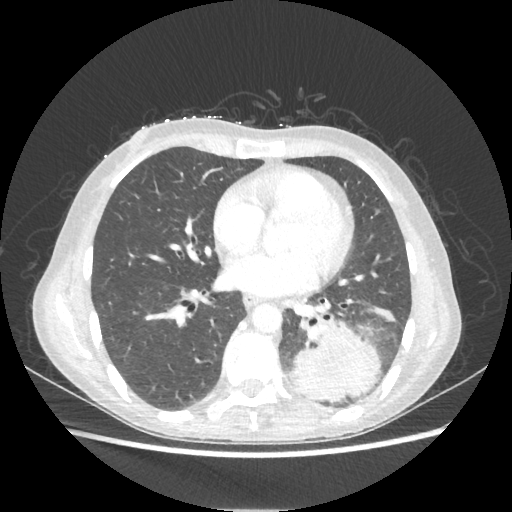
Chest CT, one axial slice. Position 96 of 221 along the scan axis. 80 kVp. Lung window (W 1500 / L -600 HU). 512 × 512 image matrix. Patient: female, 53 years. Case-level facts recorded for this patient, not image findings: clinical TNM (as recorded): T3 N0 M0.
Annotated regions visible in this slice (bounding box drawn by a radiologist):
- lung tumour (recorded histology: adenocarcinoma): bounding box [x1, y1, x2, y2] px = [287, 320, 380, 403]